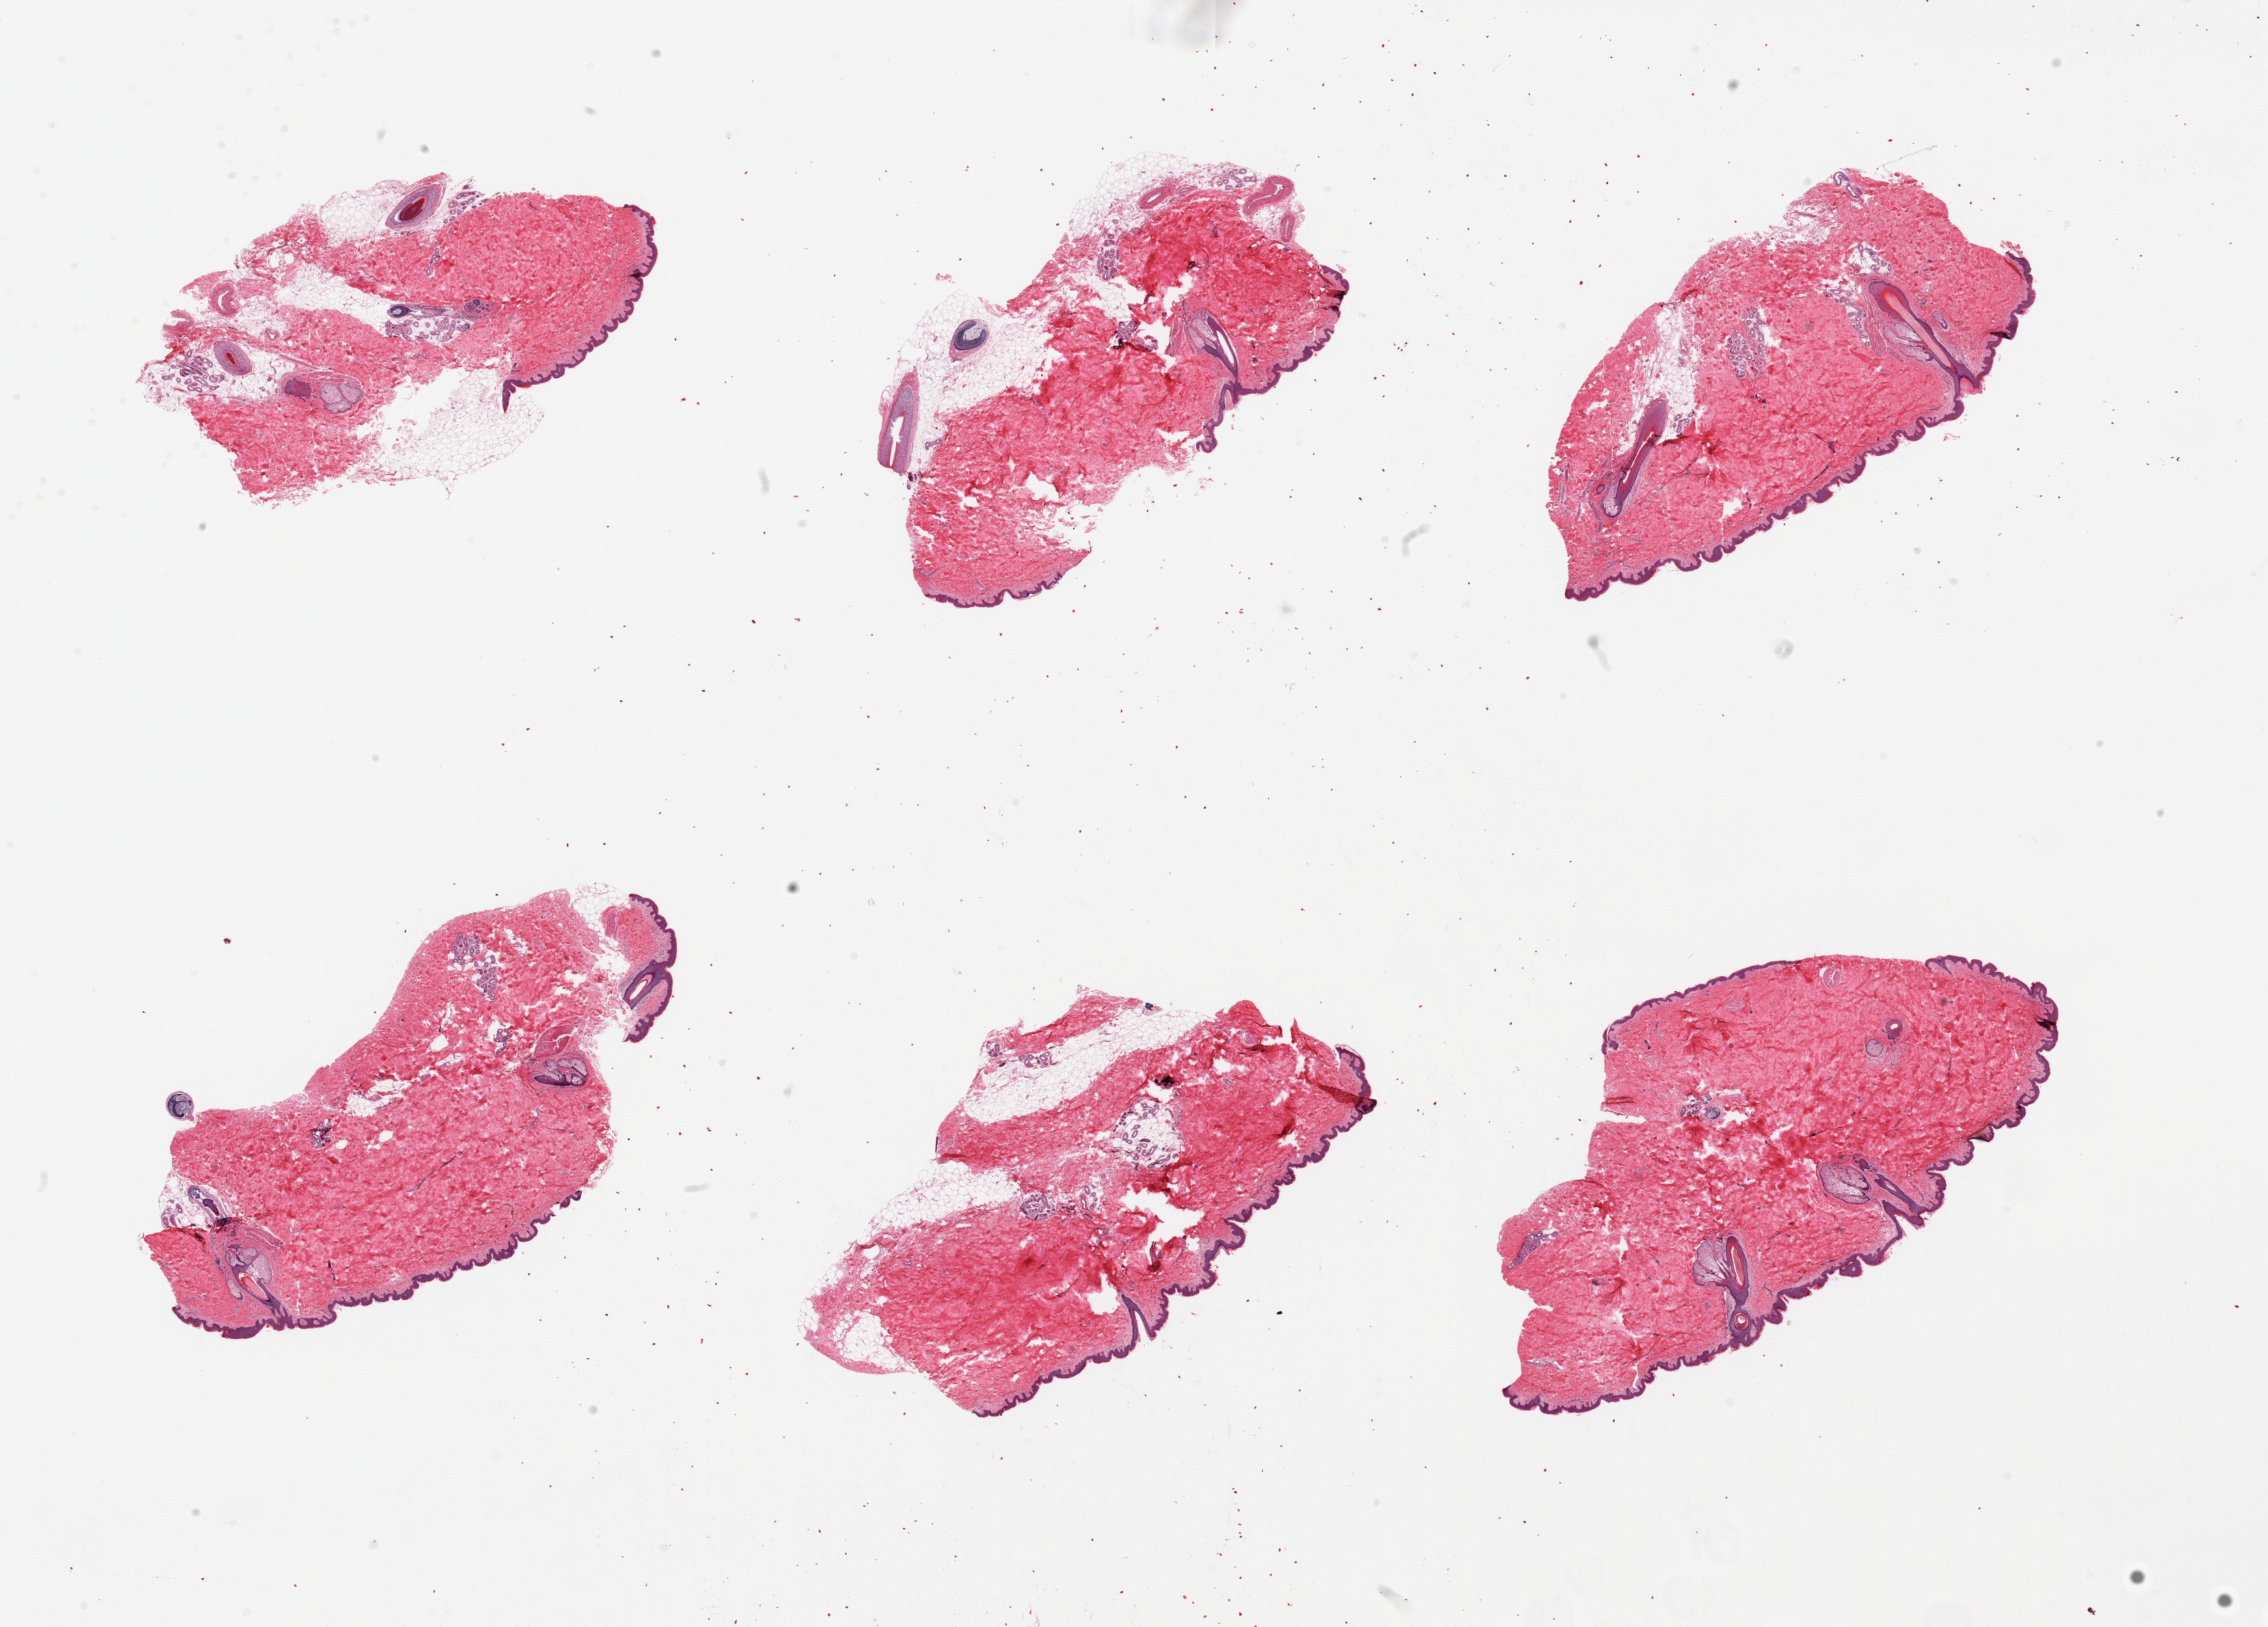
Digitized haematoxylin and eosin-stained section, brightfield — a low-resolution overview of the entire scanned area, about 27.6 x 19.8 mm (from a 20x scan); PAXgene-fixed paraffin-embedded (PFPE) section; target tissue: skin of suprapubic region; donor tissue sample. Donor sex: male.
* pathologist's review note for this sample: 6 pieces; includes from 0-20% internal and external fat